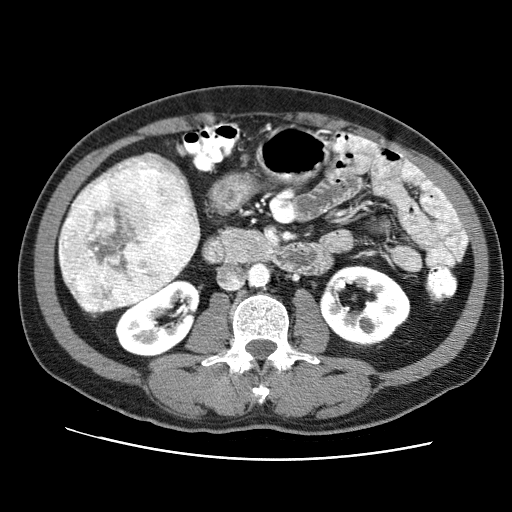
Contrast-enhanced abdominal CT (liver protocol), one axial slice; slice 22 of 71 in the series (ordered by position); reconstruction kernel STANDARD; 120 kVp; soft-tissue window (W 400 / L 40 HU); 512 × 512 image matrix, field of view 360 × 360 mm. From the clinical record (not read from this slice): diagnosis: hepatocellular carcinoma (patient treated with transarterial chemoembolisation; whether this scan precedes or follows treatment is not stated here); TNM stage (as recorded): Stage-II; Child-Pugh class: A; tumour differentiation: well differentiated.
Outlined on this slice (semi-automatic segmentation, software-assisted and operator-edited):
- liver parenchyma outside the tumour (the mass and vessels are separate outlines, so this box may not span the whole liver): bounding box (x1, y1, x2, y2) in pixels: (69, 151, 200, 312)
- mass: (58, 166, 198, 312)
- liver vessels: (119, 159, 195, 216)